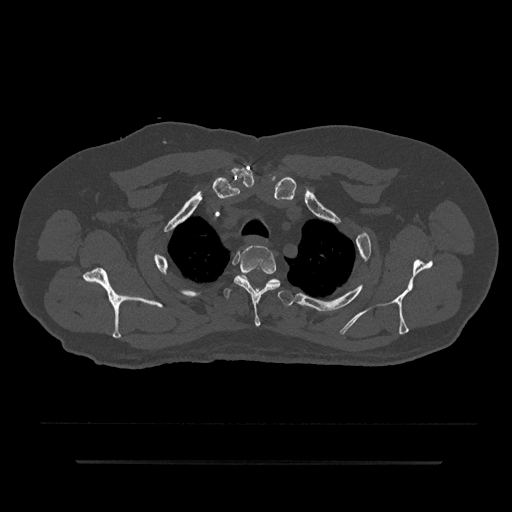
CT including the spine, one axial slice. Position 688 of 797 along the scan axis. Bone window (W 1800 / L 400 HU). 0.5 mm slice thickness. 512 × 512 image matrix, field of view 464 × 464 mm. Patient: male, 59 years. Case-level facts recorded for this patient, not image findings: primary cancer: bile ducts; vertebrae with lytic lesions (as recorded): T10.
Outlined on this slice (semi-automatically segmented with operator editing):
- T2 vertebra: bounding box <234,246,281,326> (left, top, right, bottom; pixels)
- T3 vertebra: <225,289,293,307>